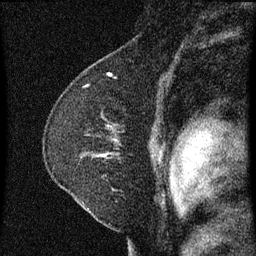
Breast MRI (dynamic contrast-enhanced), one sagittal slice; dynamic contrast-enhanced series, image 2 of 3 at this slice position (ordered by acquisition); 1.5 T; TE 4.2 ms, TR 8 ms; 2 mm slice thickness; 256 × 256 image matrix, field of view 180 × 180 mm. Female patient, age 47 years.
Structures marked on this image (semi-automatic segmentation, software-assisted and operator-edited):
- analysis volume of interest (the breast-tissue region the enhancement analysis was run in; not a lesion): bounding box (x1, y1, x2, y2) in pixels: (45, 100, 158, 213)
- tumour enhancement mask (voxels above the 70 % enhancement threshold inside the analysis volume of interest): (101, 154, 107, 157)